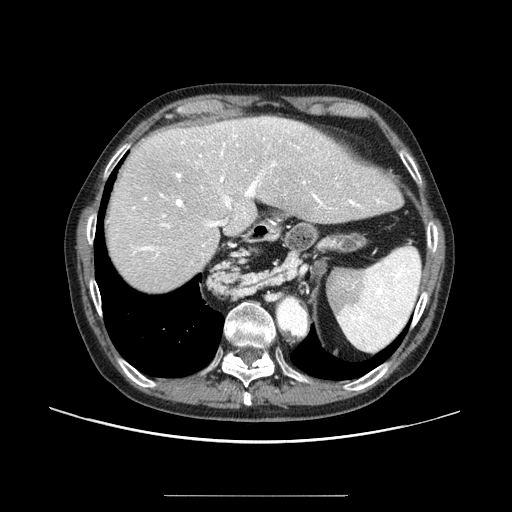
Contrast-enhanced abdominal CT (liver protocol), one axial slice. Position 69 of 91 along the scan axis. 100 kVp. One of 2 acquisitions stored at this slice position. Soft-tissue window (W 400 / L 40 HU). 512 × 512 image matrix, field of view 400 × 400 mm. From the clinical record (not read from this slice): diagnosis: hepatocellular carcinoma (patient treated with transarterial chemoembolisation; whether this scan precedes or follows treatment is not stated here); TNM stage (as recorded): Stage-I; Child-Pugh class: A; tumour differentiation: moderately differentiated; tumour nodularity: uninodular.
Annotated regions visible in this slice (semi-automatically segmented with operator editing):
- abdominal aorta: bounding box (x1, y1, x2, y2) in pixels: (278, 299, 306, 335)
- liver parenchyma outside the tumour (the mass and vessels are separate outlines, so this box may not span the whole liver): (106, 116, 400, 292)
- mass: (150, 138, 177, 163)
- liver vessels: (132, 118, 380, 256)